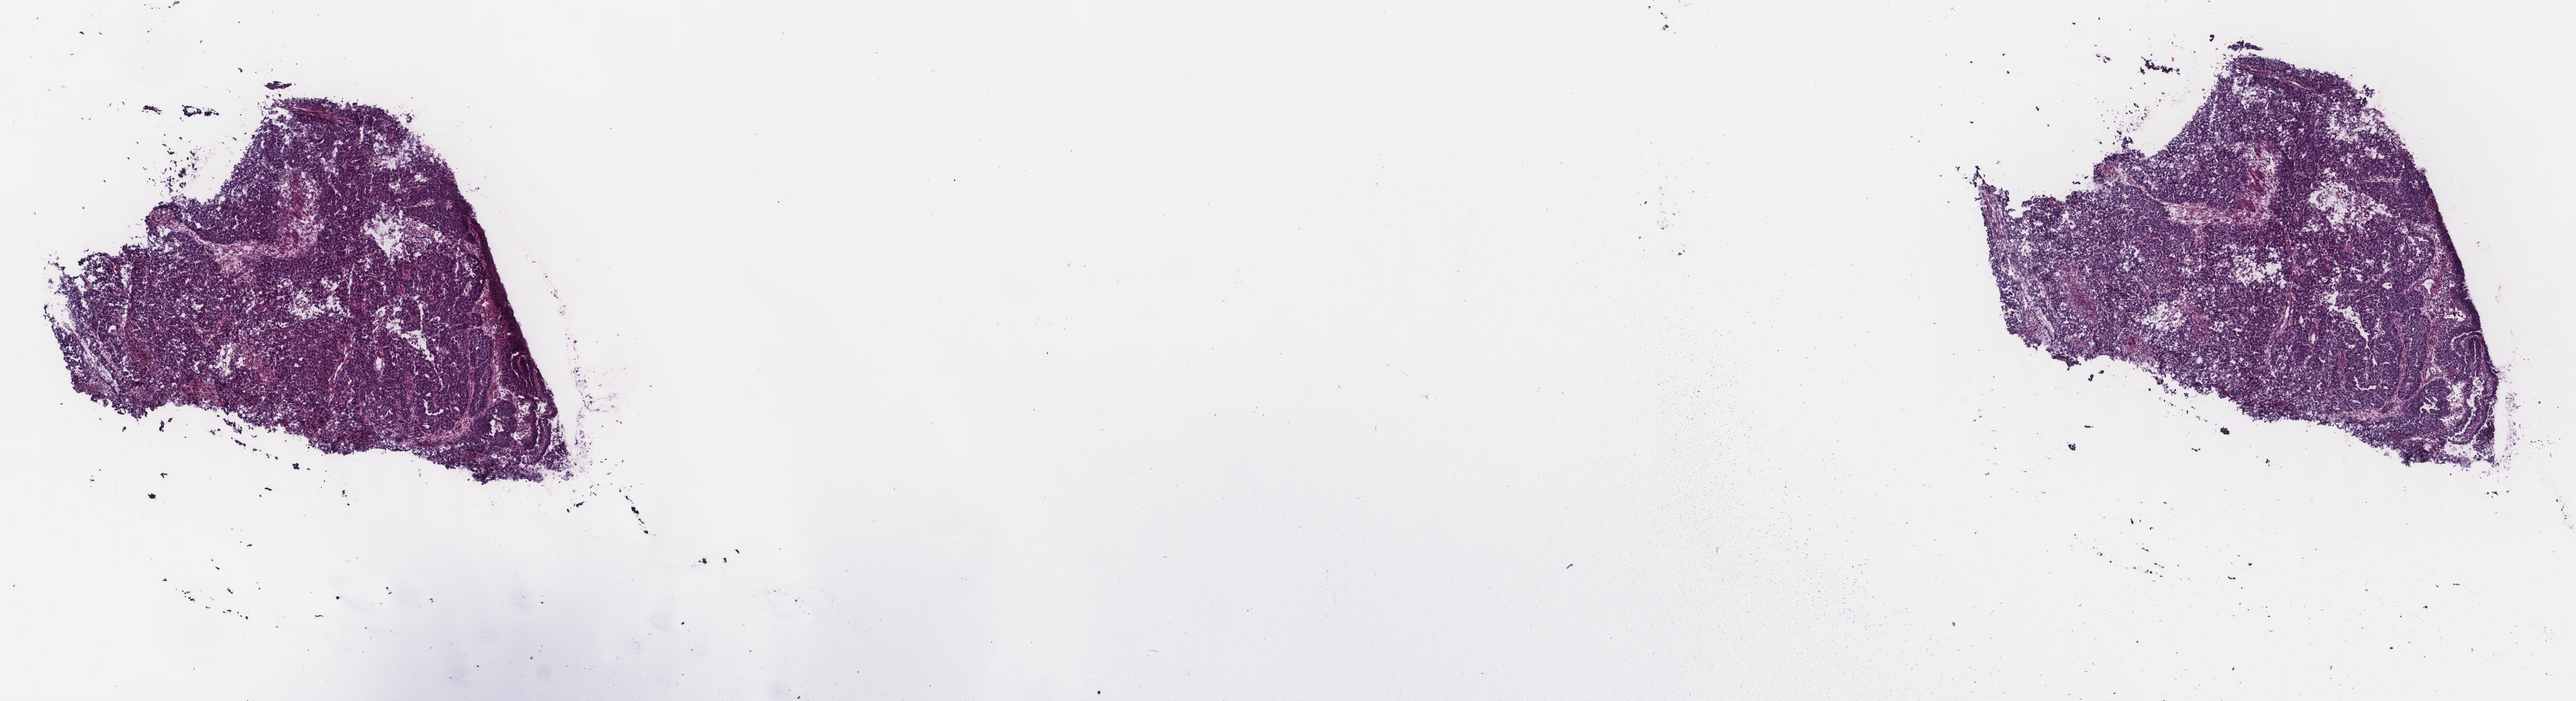
Digitized H&E tissue section (whole slide), shown as a low-resolution overview of the whole scanned area (about 15.1 x 4.1 mm). Frozen section. Sample: primary tumour, uterus. Female, age 67 years at initial diagnosis. Histologic grade: G3 (poorly differentiated). Slide review estimates, as recorded: tumour cells 86%, tumour nuclei 90%, normal cells 0%, stromal cells 10%, necrosis 4%. Inflammatory infiltration, as recorded: lymphocyte infiltration 3%, monocyte infiltration 8%, neutrophil infiltration 5%.
• histologic diagnosis: Serous cystadenocarcinoma, NOS
• FIGO stage: II